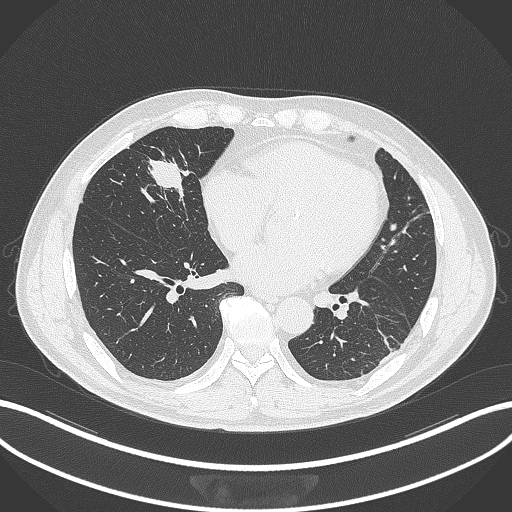
Chest CT, one axial slice. Slice 108 of 399 in the series (ordered by position). Lung window (W 1500 / L -600 HU). 1 mm slice thickness. 512 × 512 image matrix, field of view 400 × 400 mm. Patient: male, 59 years. Case-level facts recorded for this patient, not image findings: clinical TNM (as recorded): T2a N1 M0.
Structures marked on this image (bounding box drawn by a radiologist):
- lung tumour (recorded histology: adenocarcinoma): box from (x=138, y=152) to (x=191, y=205) px